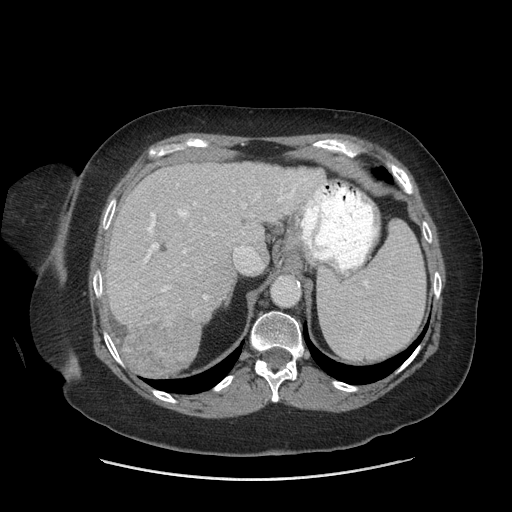
Contrast-enhanced abdominal CT (liver protocol), one axial slice. Slice 51 of 69 in the series (ordered by position). 140 kVp. Soft-tissue window (W 400 / L 40 HU). 2.5 mm slice thickness. 512 × 512 image matrix, field of view 420 × 420 mm. Case-level facts recorded for this patient, not image findings: diagnosis: hepatocellular carcinoma (patient treated with transarterial chemoembolisation; whether this scan precedes or follows treatment is not stated here); TNM stage (as recorded): Stage-IIIB; Child-Pugh class: A; tumour differentiation: moderately differentiated.
Structures marked on this image (semi-automatically segmented with operator editing):
- liver parenchyma outside the tumour (the mass and vessels are separate outlines, so this box may not span the whole liver): bounding box <104,162,322,376> (left, top, right, bottom; pixels)
- mass: <122,305,200,376>
- liver vessels: <144,178,307,300>